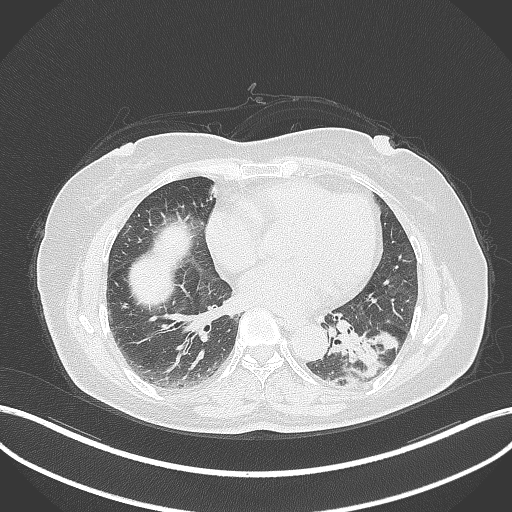
Chest CT, one axial slice. Position 155 of 311 along the scan axis. Reconstruction kernel B70f. 120 kVp. Lung window (W 1500 / L -600 HU). 1 mm slice thickness. 512 × 512 image matrix. Patient: female, 59 years. Case-level facts recorded for this patient, not image findings: clinical TNM (as recorded): T2a N0 M0.
Annotated regions visible in this slice (rectangle marked by the reading radiologist):
- lung tumour (recorded histology: adenocarcinoma): bounding box [x1, y1, x2, y2] px = [348, 330, 403, 384]